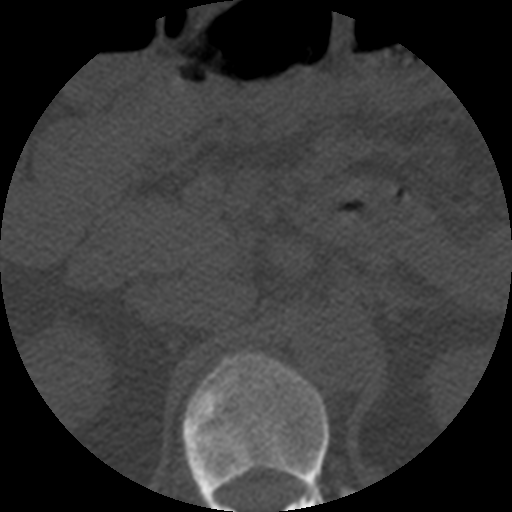
CT including the spine, one axial slice; slice 208 of 508 in the series (ordered by position); bone window (W 1800 / L 400 HU); 1.25 mm slice thickness; 512 × 512 image matrix. Patient age 57 years. Case-level facts recorded for this patient, not image findings: primary cancer: prostate.
Structures marked on this image (semi-automatic segmentation, software-assisted and operator-edited):
- T12 vertebra: bounding box [x1, y1, x2, y2] px = [182, 352, 330, 512]